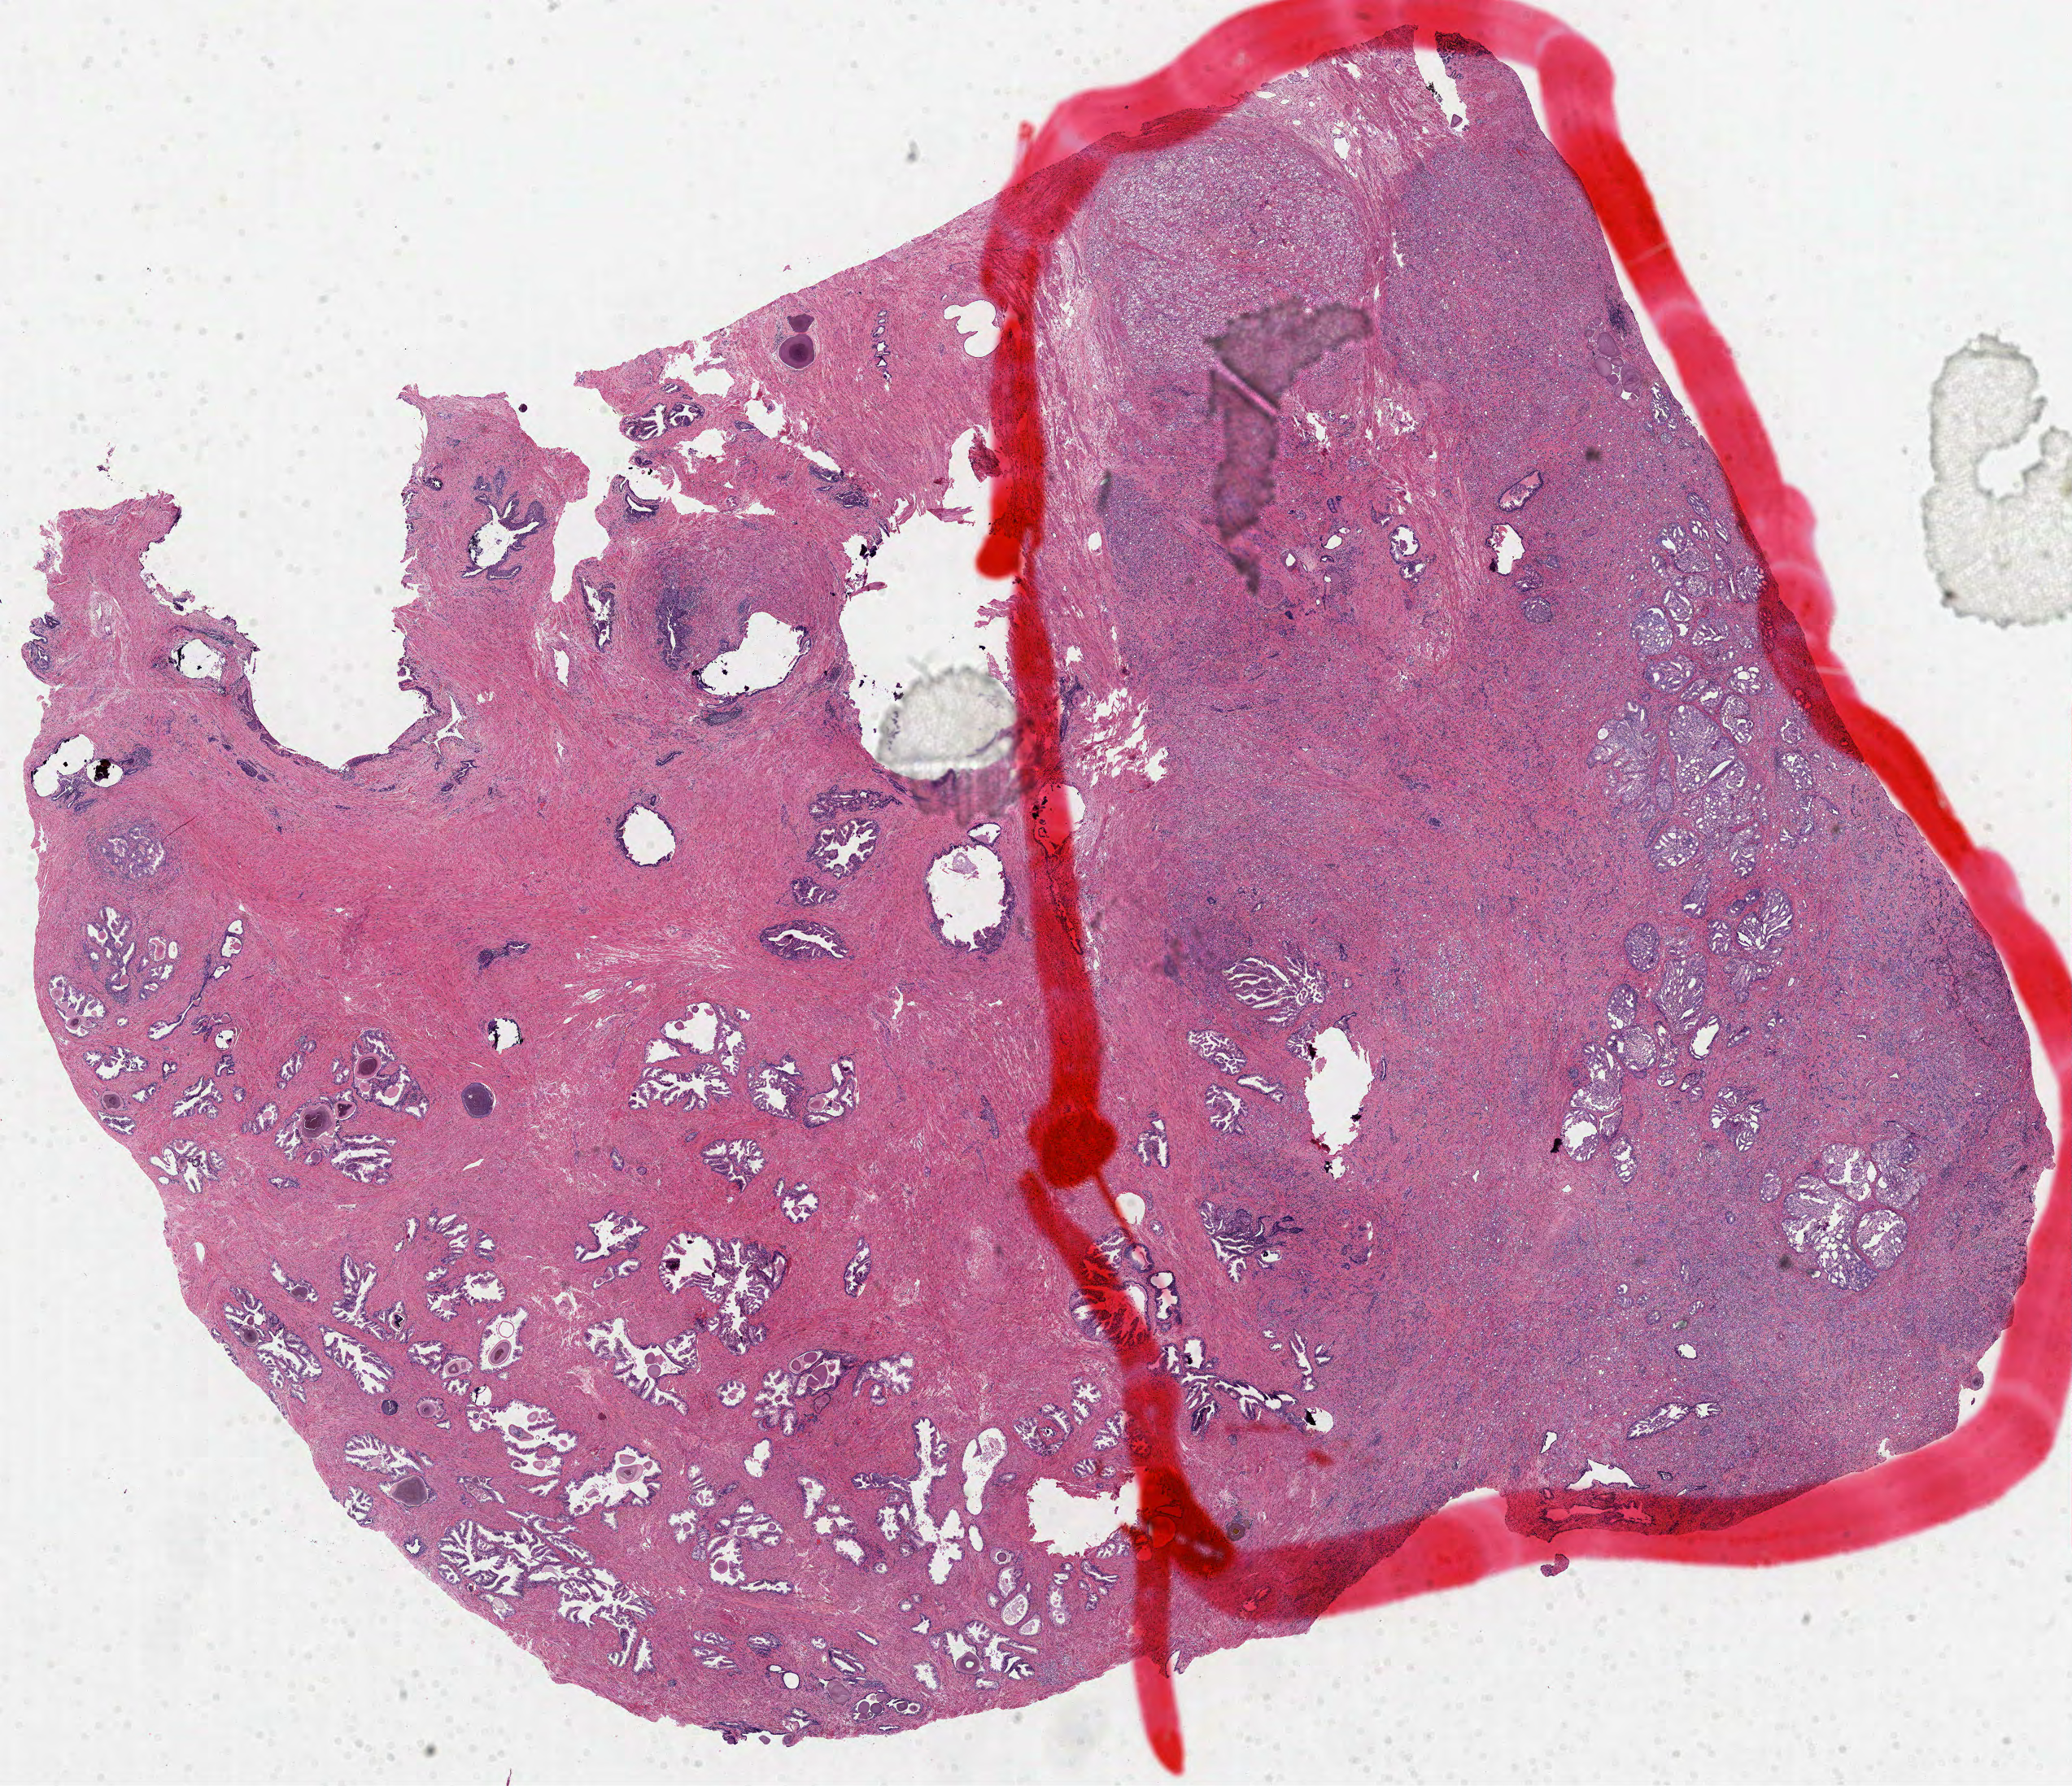
H&E whole-slide image, whole scanned area (about 20.5 x 17.7 mm, from a 40x scan) shown as a low-resolution overview. FFPE section. Primary tumour sample from the prostate. Male patient; age at initial diagnosis 57 years.
Pathologic diagnosis: Acinar cell carcinoma (prostate gland).